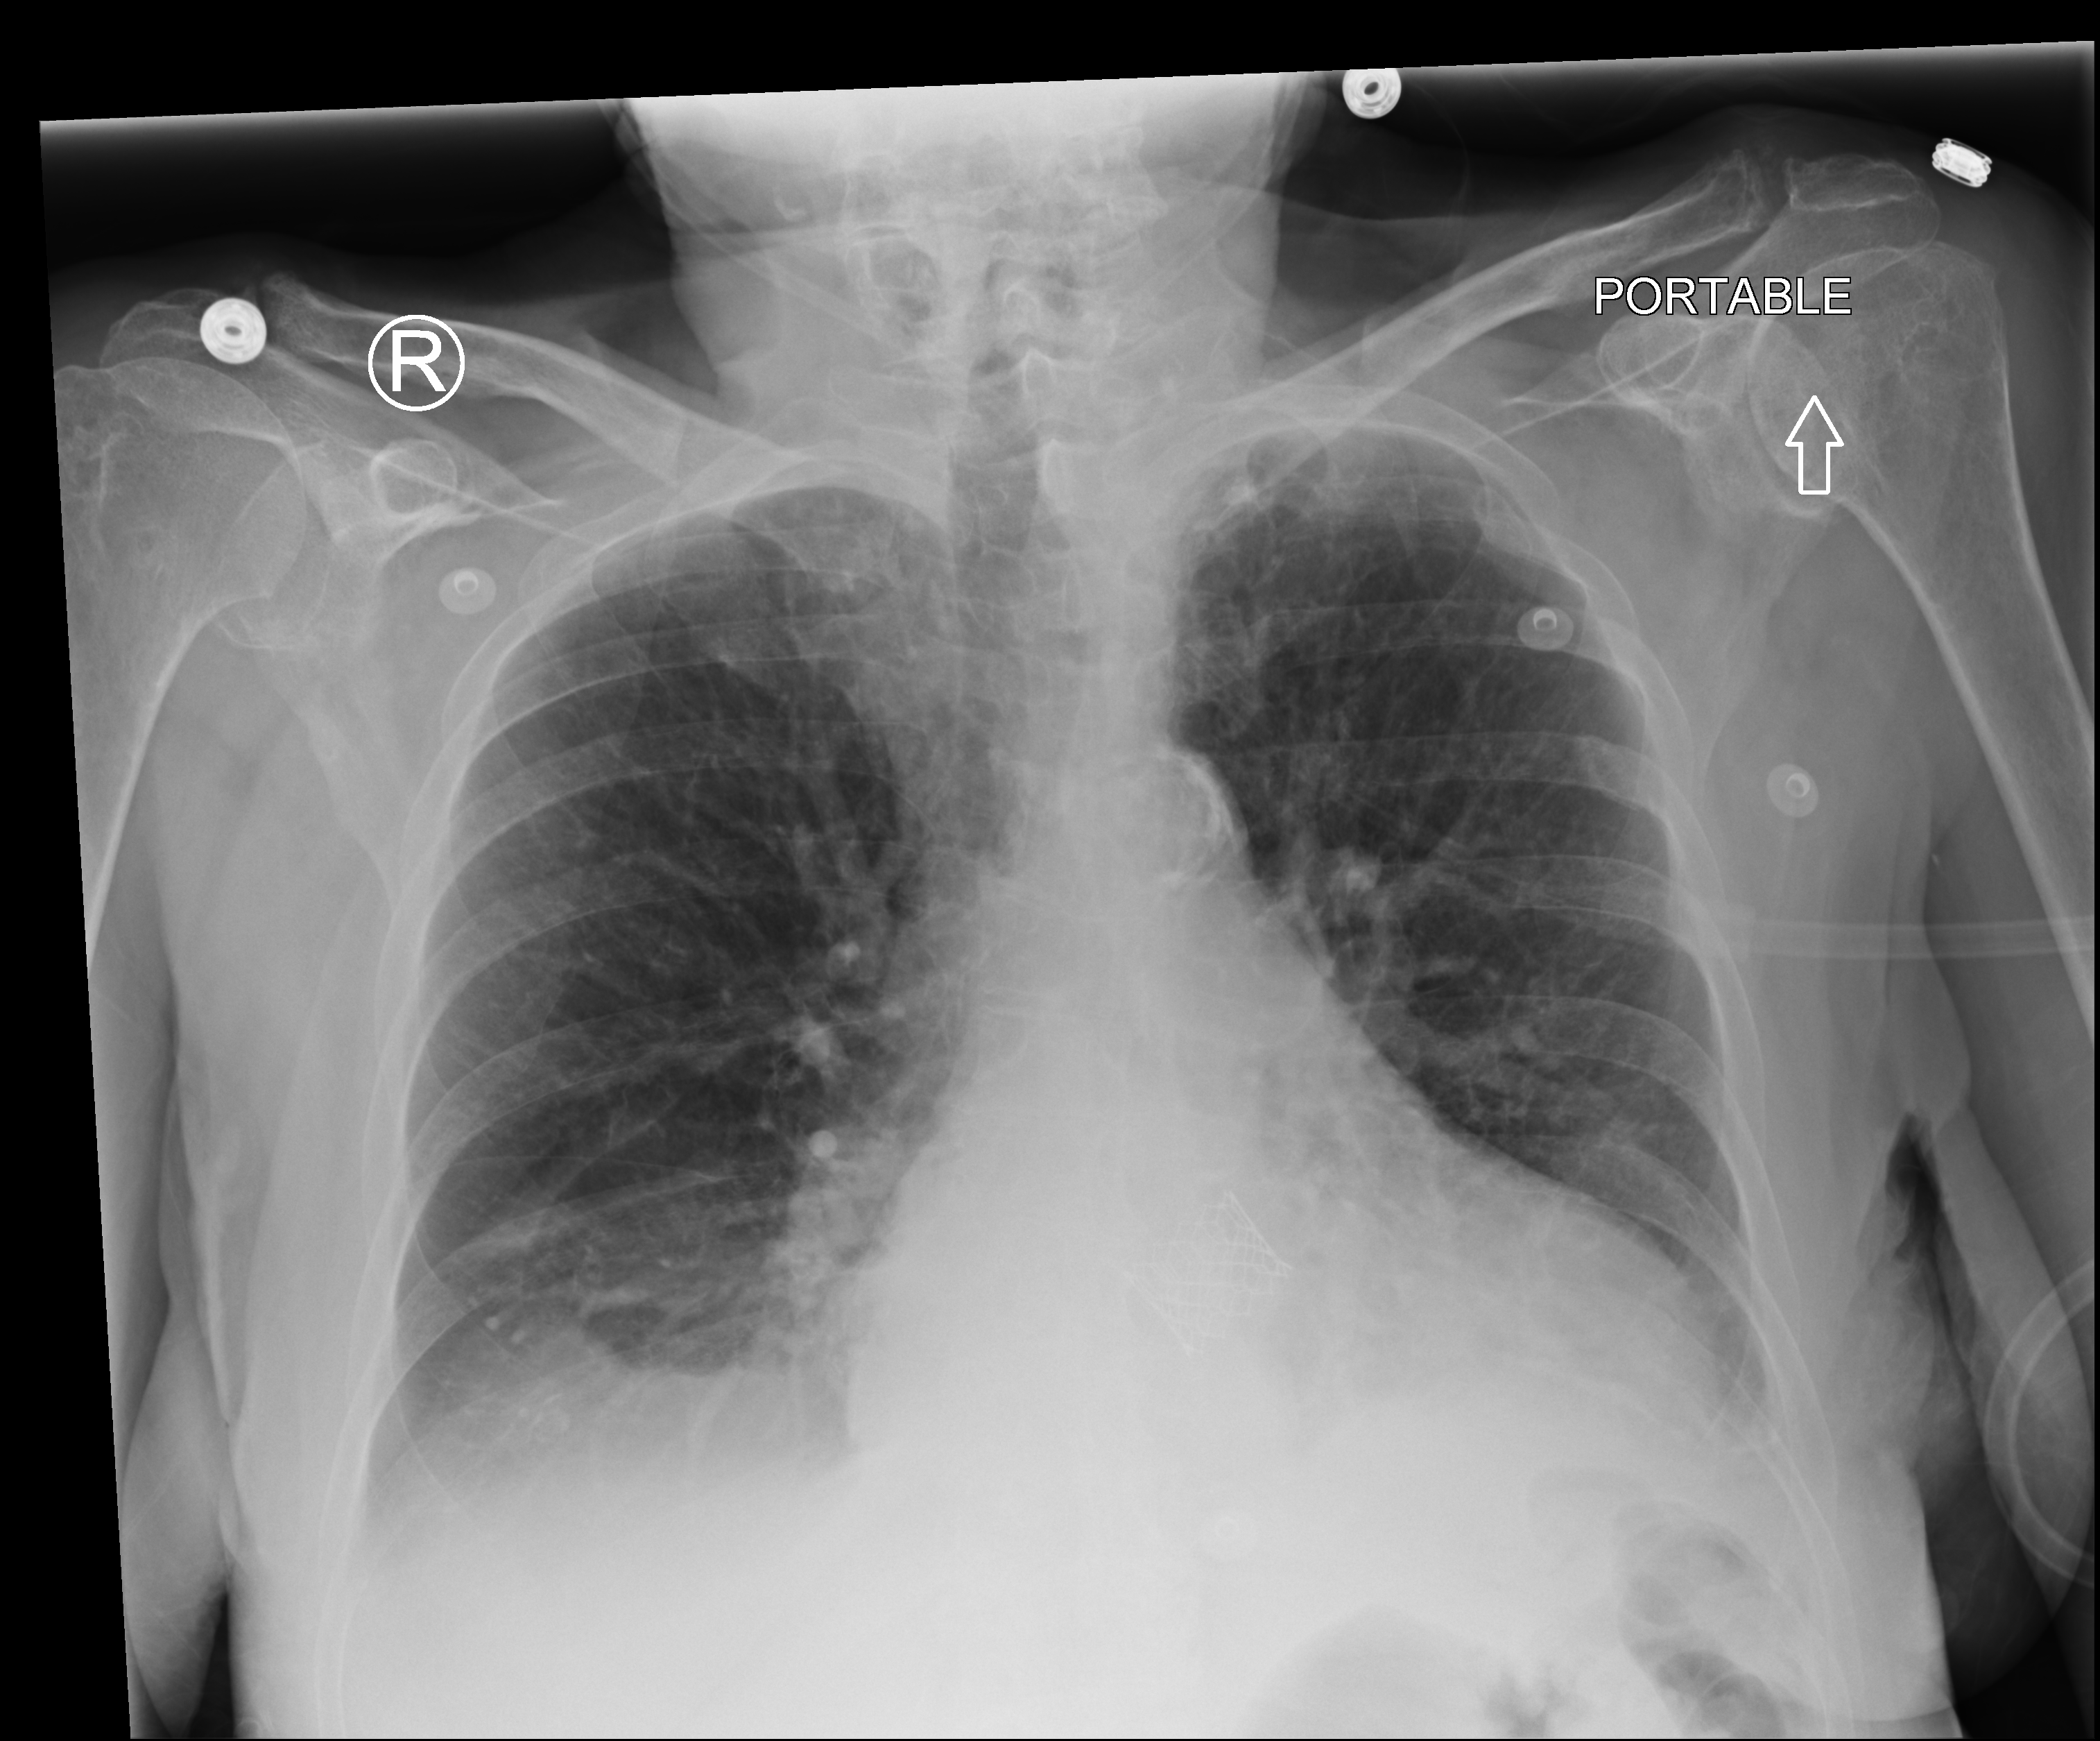
Portable chest radiograph, anteroposterior (AP) projection. Female patient hospitalised with COVID-19, age 75–90 years.
Hospital-stay facts (about this admission, not read from this image; timing relative to this image not recorded):
- mechanically ventilated during this hospital stay: no